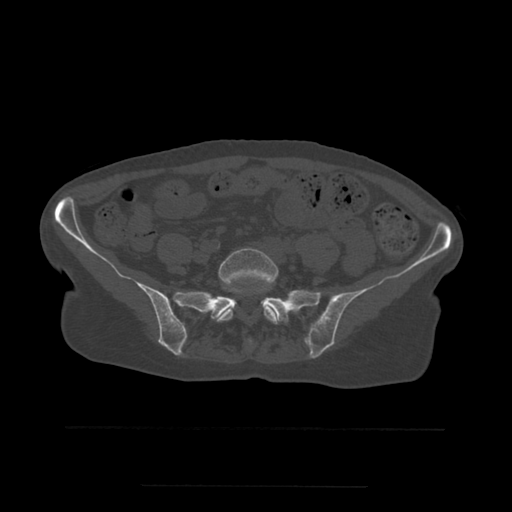
CT including the spine, one axial slice. Position 136 of 544 along the scan axis. Bone window (W 1800 / L 400 HU). 512 × 512 image matrix, field of view 350 × 350 mm. Patient age 58 years. Case-level facts recorded for this patient, not image findings: primary cancer: lung.
Structures marked on this image (semi-automatic segmentation, software-assisted and operator-edited):
- L5 vertebra: box from (x=217, y=248) to (x=279, y=325) px